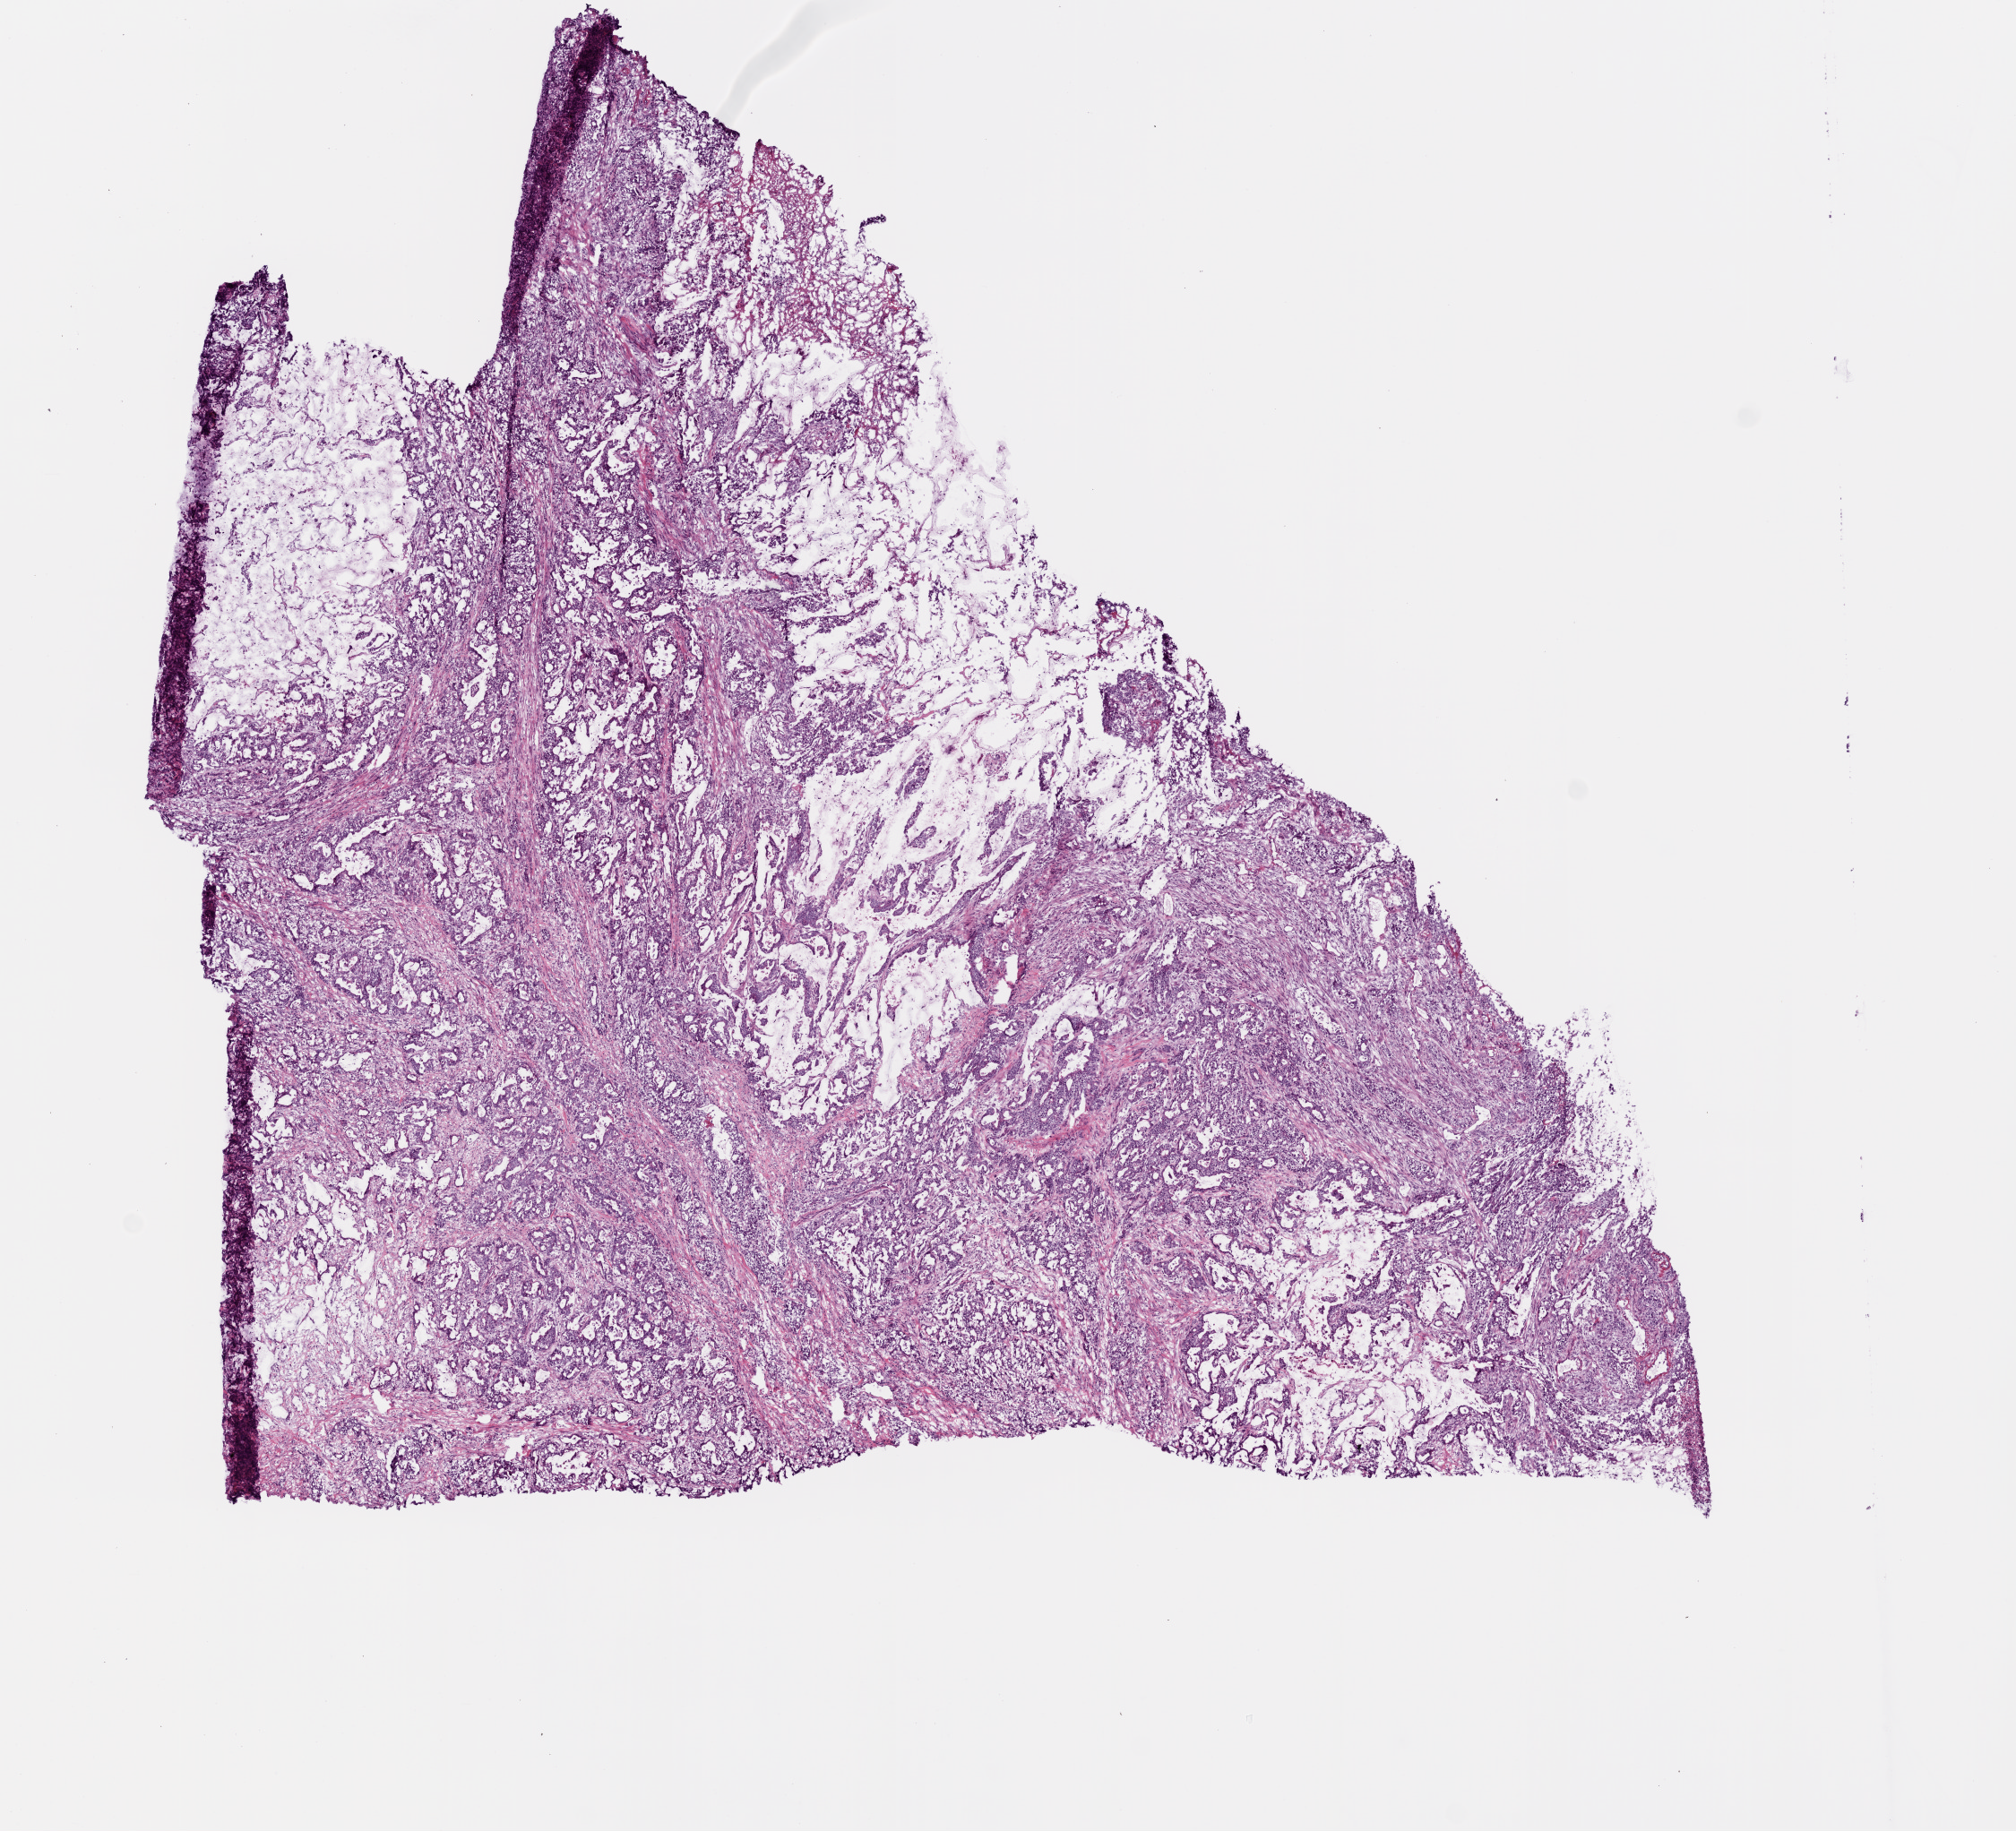
Digitized H&E tissue section (whole slide), low-resolution overview of the scanned area, about 9.0 x 8.2 mm (from a 20x scan), frozen section, sample: primary tumour, stomach. Female, age 83 years at initial diagnosis. Histologic grade: G3 (poorly differentiated). Pathologist review of this section (percent, as recorded): tumour cells 85%, tumour nuclei 80%, normal cells 0%, stromal cells 15%, necrosis 0%.
• lymph nodes positive (case pathology): 7 of 32 examined
• histologic diagnosis: Adenocarcinoma, intestinal type (gastric antrum)
• AJCC pathologic stage: IIIA (5th edition)